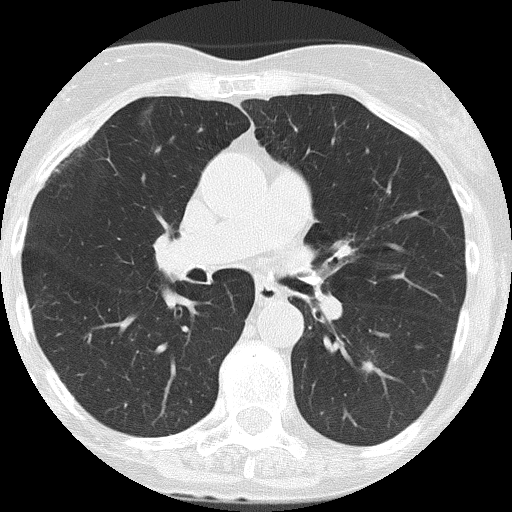
Chest CT (low-dose screening protocol), one axial image; second screening round (one year after baseline); lung window (W 1500 / L -600 HU); 2 mm slice thickness; lung (sharp) reconstruction kernel (FC51); 512 × 512 image matrix. Female participant, aged 68 years at enrolment. Former smoker at enrolment.
• Lesion marked by an expert reader, bounding box <346,344,392,390> (left, top, right, bottom; pixels).
• Screening reader's record for this exam: no non-calcified nodule ≥4 mm recorded.
• Official screen result: negative screen, no significant abnormalities.
• Later outcome: lung cancer diagnosed 535 days after this screen (after the third annual screen) — non-small cell carcinoma, left lower lobe, poorly differentiated (G3), stage IA (AJCC 6th edition), 10 mm at pathology.